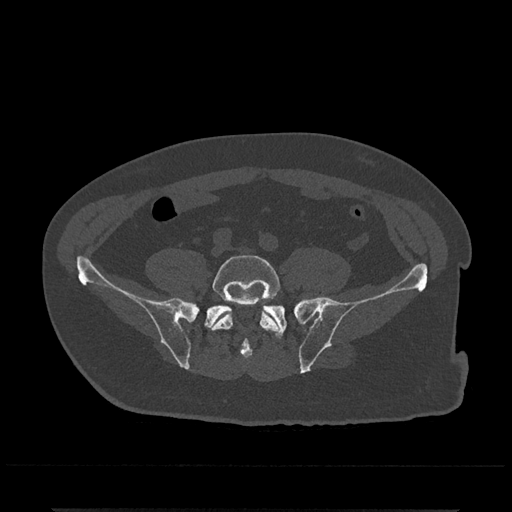
CT including the spine, one axial slice; slice 64 of 797 in the series (ordered by position); reconstruction kernel Br40s/3; 120 kVp; bone window (W 1800 / L 400 HU); 0.5 mm slice thickness; 512 × 512 image matrix. Patient: male, 67 years. From the clinical record (not read from this slice): primary cancer: prostate.
Outlined on this slice (semi-automatic segmentation, software-assisted and operator-edited):
- L5 vertebra: bounding box (x1, y1, x2, y2) in pixels: (210, 255, 280, 334)